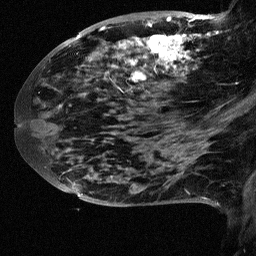
Breast MRI (dynamic contrast-enhanced), one sagittal slice; slice 28 of 64 in the series (ordered by position); dynamic contrast-enhanced study with each time point stored as its own series, time point 2 of 3 at this slice position (early post-contrast, ordered by acquisition time); 1.5 T; TE 4.5 ms, TR 11 ms; 256 × 256 image matrix, field of view 200 × 200 mm. Female patient, age 38 years. From the clinical record (not read from this slice): setting: breast cancer imaged before/during neoadjuvant chemotherapy; receptor status: HR-positive, HER2-negative.
Structures marked on this image (semi-automatically segmented with operator editing):
- analysis volume of interest (the breast-tissue region the enhancement analysis was run in; not a lesion): bounding box <88,18,252,126> (left, top, right, bottom; pixels)
- tumour enhancement mask (voxels above the 90 % enhancement threshold inside the analysis volume of interest): <111,18,219,83>